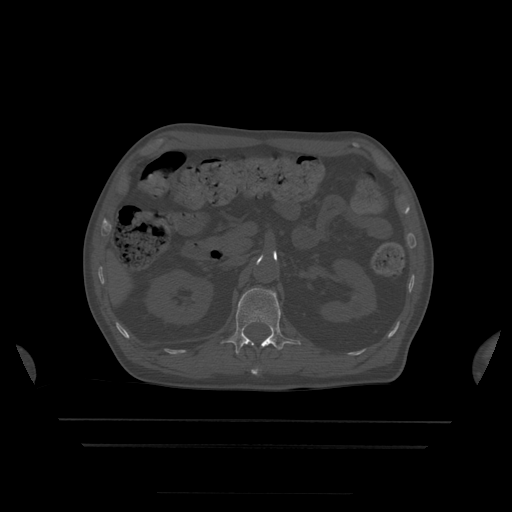
CT including the spine, one axial slice. Slice 173 of 522 in the series (ordered by position). Bone window (W 1800 / L 400 HU). 512 × 512 image matrix, field of view 436 × 436 mm. Patient age 68 years. Case-level facts recorded for this patient, not image findings: primary cancer: urothelial.
Structures marked on this image (semi-automatic segmentation, software-assisted and operator-edited):
- L1 vertebra: box from (x=222, y=288) to (x=301, y=355) px
- T12 vertebra: (x=251, y=369)–(x=259, y=375)